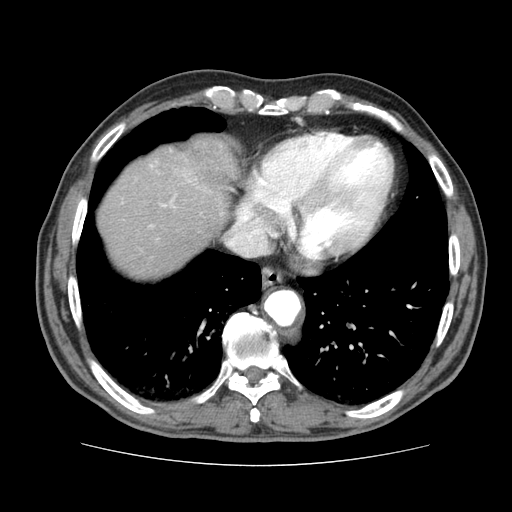
Contrast-enhanced abdominal CT (liver protocol), one axial slice; slice 71 of 79 in the series (ordered by position); reconstruction kernel STANDARD; 120 kVp; soft-tissue window (W 400 / L 40 HU); 2.5 mm slice thickness; 512 × 512 image matrix, field of view 360 × 360 mm. Case-level facts recorded for this patient, not image findings: diagnosis: hepatocellular carcinoma (patient treated with transarterial chemoembolisation; whether this scan precedes or follows treatment is not stated here); TNM stage (as recorded): Stage-I; Child-Pugh class: A.
Annotated regions visible in this slice (semi-automatically segmented with operator editing):
- abdominal aorta: bounding box (x1, y1, x2, y2) in pixels: (267, 291, 302, 325)
- liver parenchyma outside the tumour (the mass and vessels are separate outlines, so this box may not span the whole liver): (98, 138, 231, 278)
- mass: (155, 134, 239, 199)
- liver vessels: (150, 165, 174, 226)